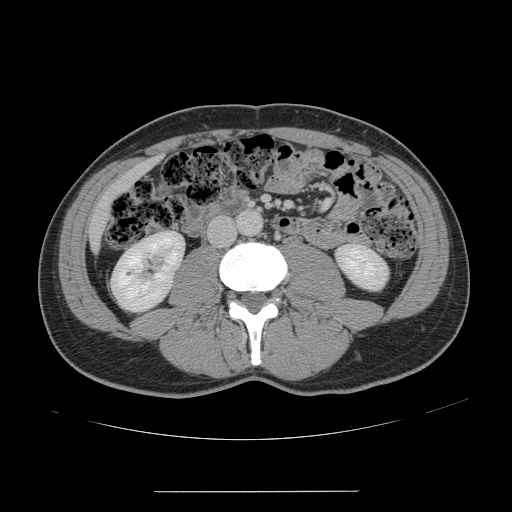
Contrast-enhanced abdominal CT, one axial slice. Slice 31 of 178 in the series (ordered by position). Intravenous contrast given. Soft-tissue window (W 400 / L 40 HU). 2.5 mm slice thickness. 512 × 512 image matrix, field of view 401 × 401 mm. Male patient, age 53 years. From the clinical record (not read from this slice): diagnosis: colorectal cancer liver metastases, imaged before liver resection; multiple liver metastases: yes; largest metastasis: 2.4 cm.
Outlined on this slice (manually delineated by an expert):
- liver: box from (x=91, y=159) to (x=155, y=248) px